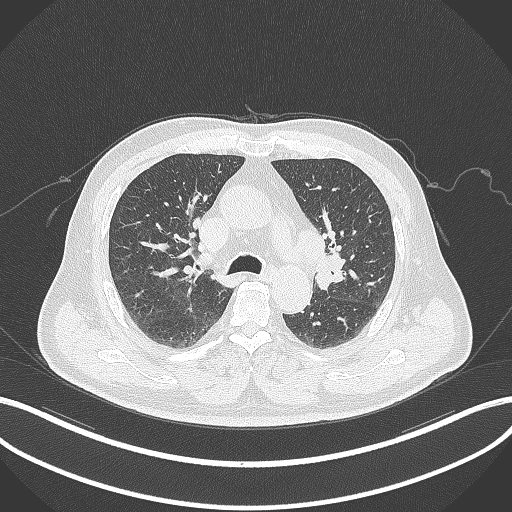
Chest CT, one axial slice. Slice 195 of 286 in the series (ordered by position). Reconstruction kernel B70f. Lung window (W 1500 / L -600 HU). 512 × 512 image matrix, field of view 400 × 400 mm. Male patient, age 67 years. From the clinical record (not read from this slice): clinical TNM (as recorded): T2a N1 M0.
Outlined on this slice (rectangle marked by the reading radiologist):
- lung tumour (recorded histology: adenocarcinoma): bounding box <324,251,345,285> (left, top, right, bottom; pixels)